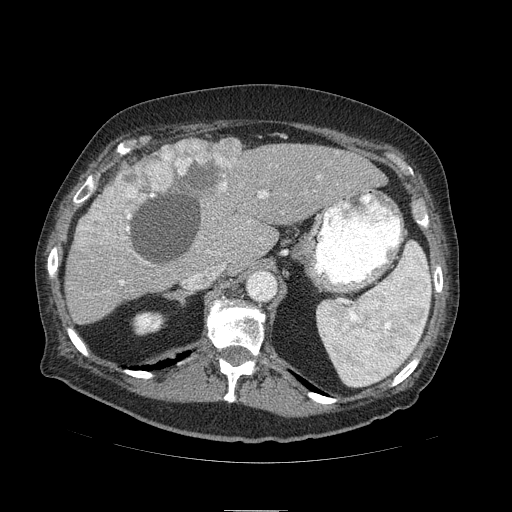
Contrast-enhanced abdominal CT (liver protocol), one axial slice; slice 64 of 103 in the series (ordered by position); 120 kVp; soft-tissue window (W 400 / L 40 HU); 512 × 512 image matrix, field of view 440 × 440 mm. Case-level facts recorded for this patient, not image findings: diagnosis: hepatocellular carcinoma (patient treated with transarterial chemoembolisation; whether this scan precedes or follows treatment is not stated here); TNM stage (as recorded): Stage-IIIA; Child-Pugh class: B; tumour nodularity: multinodular.
Structures marked on this image (semi-automatic segmentation, software-assisted and operator-edited):
- liver parenchyma outside the tumour (the mass and vessels are separate outlines, so this box may not span the whole liver): bounding box (x1, y1, x2, y2) in pixels: (64, 140, 386, 324)
- mass: (79, 137, 242, 250)
- liver vessels: (120, 191, 267, 283)